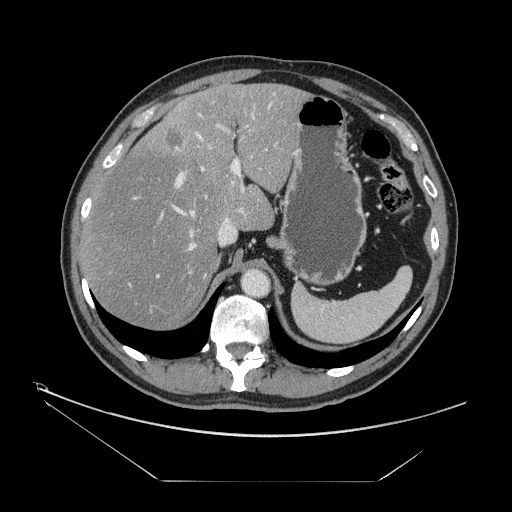
Contrast-enhanced abdominal CT, one axial slice. Position 107 of 161 along the scan axis. Reconstruction kernel STANDARD. Intravenous contrast given. Soft-tissue window (W 400 / L 40 HU). 512 × 512 image matrix, field of view 440 × 440 mm. Male patient, age 65 years. From the clinical record (not read from this slice): diagnosis: colorectal cancer liver metastases, imaged before liver resection; multiple liver metastases: yes; largest metastasis: 4.2 cm; disease in both lobes: yes.
Annotated regions visible in this slice (outlined manually by an expert reader):
- hepatic veins: bounding box [x1, y1, x2, y2] px = [129, 133, 235, 285]
- liver: [83, 84, 305, 329]
- planned liver remnant (the part of the liver to remain after resection): [83, 84, 304, 329]
- portal vein (with intrahepatic branches): [133, 92, 275, 312]
- liver metastasis: [167, 133, 185, 150]